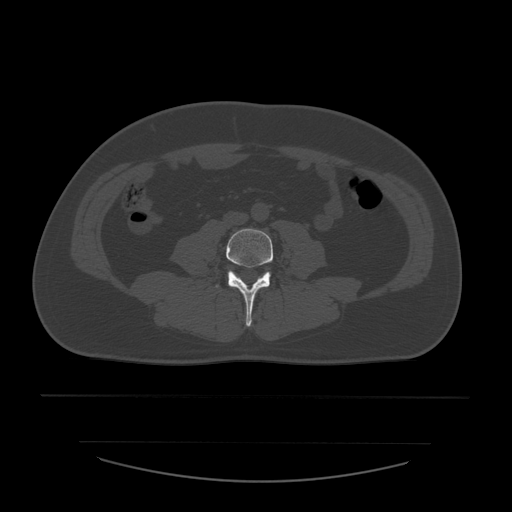
CT including the spine, one axial slice. Slice 145 of 532 in the series (ordered by position). Reconstruction kernel STANDARD. 120 kVp. Bone window (W 1800 / L 400 HU). 512 × 512 image matrix, field of view 441 × 441 mm. Patient age 44 years. From the clinical record (not read from this slice): primary cancer: soft tissue sarcoma.
Annotated regions visible in this slice (semi-automatic segmentation, software-assisted and operator-edited):
- L4 vertebra: bounding box (x1, y1, x2, y2) in pixels: (216, 229, 274, 327)